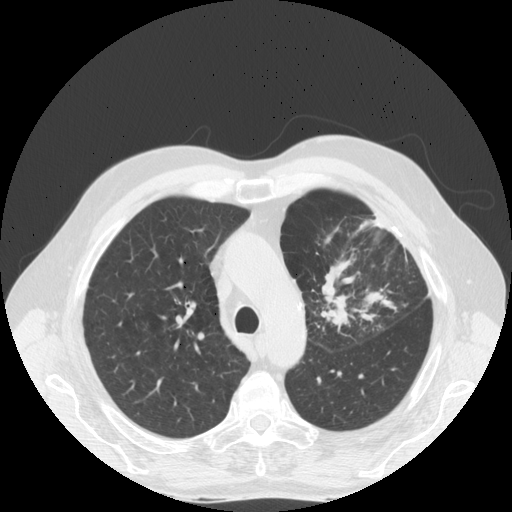
Low-dose screening chest CT, one axial slice; slice 125 of 170 in the series (ordered by position); reconstruction kernel STANDARD; 140 kVp; lung window (W 1500 / L -600 HU); 512 × 512 image matrix, field of view 380 × 380 mm.
Outlined on this slice (outlined manually by an expert reader):
- lesion 1 (tumor, upper lobe of left lung): bounding box <326,291,354,327> (left, top, right, bottom; pixels)